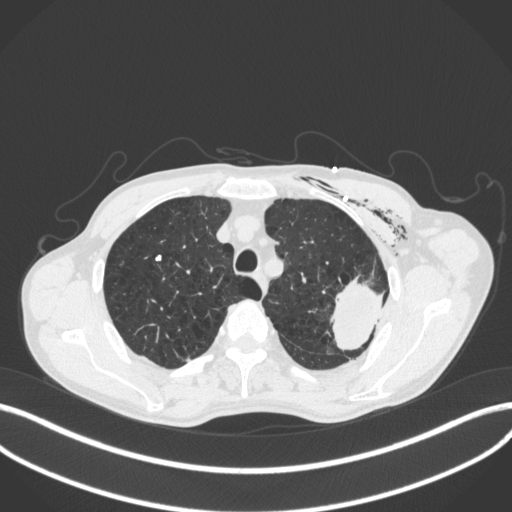
Chest CT, one axial slice; slice 326 of 416 in the series (ordered by position); reconstruction kernel B31f; 120 kVp; lung window (W 1500 / L -600 HU); 1 mm slice thickness; 512 × 512 image matrix. Male patient, age 58 years. From the clinical record (not read from this slice): clinical TNM (as recorded): T3 N0 M0.
Structures marked on this image (bounding box drawn by a radiologist):
- lung tumour (recorded histology: adenocarcinoma): box from (x=330, y=271) to (x=398, y=355) px